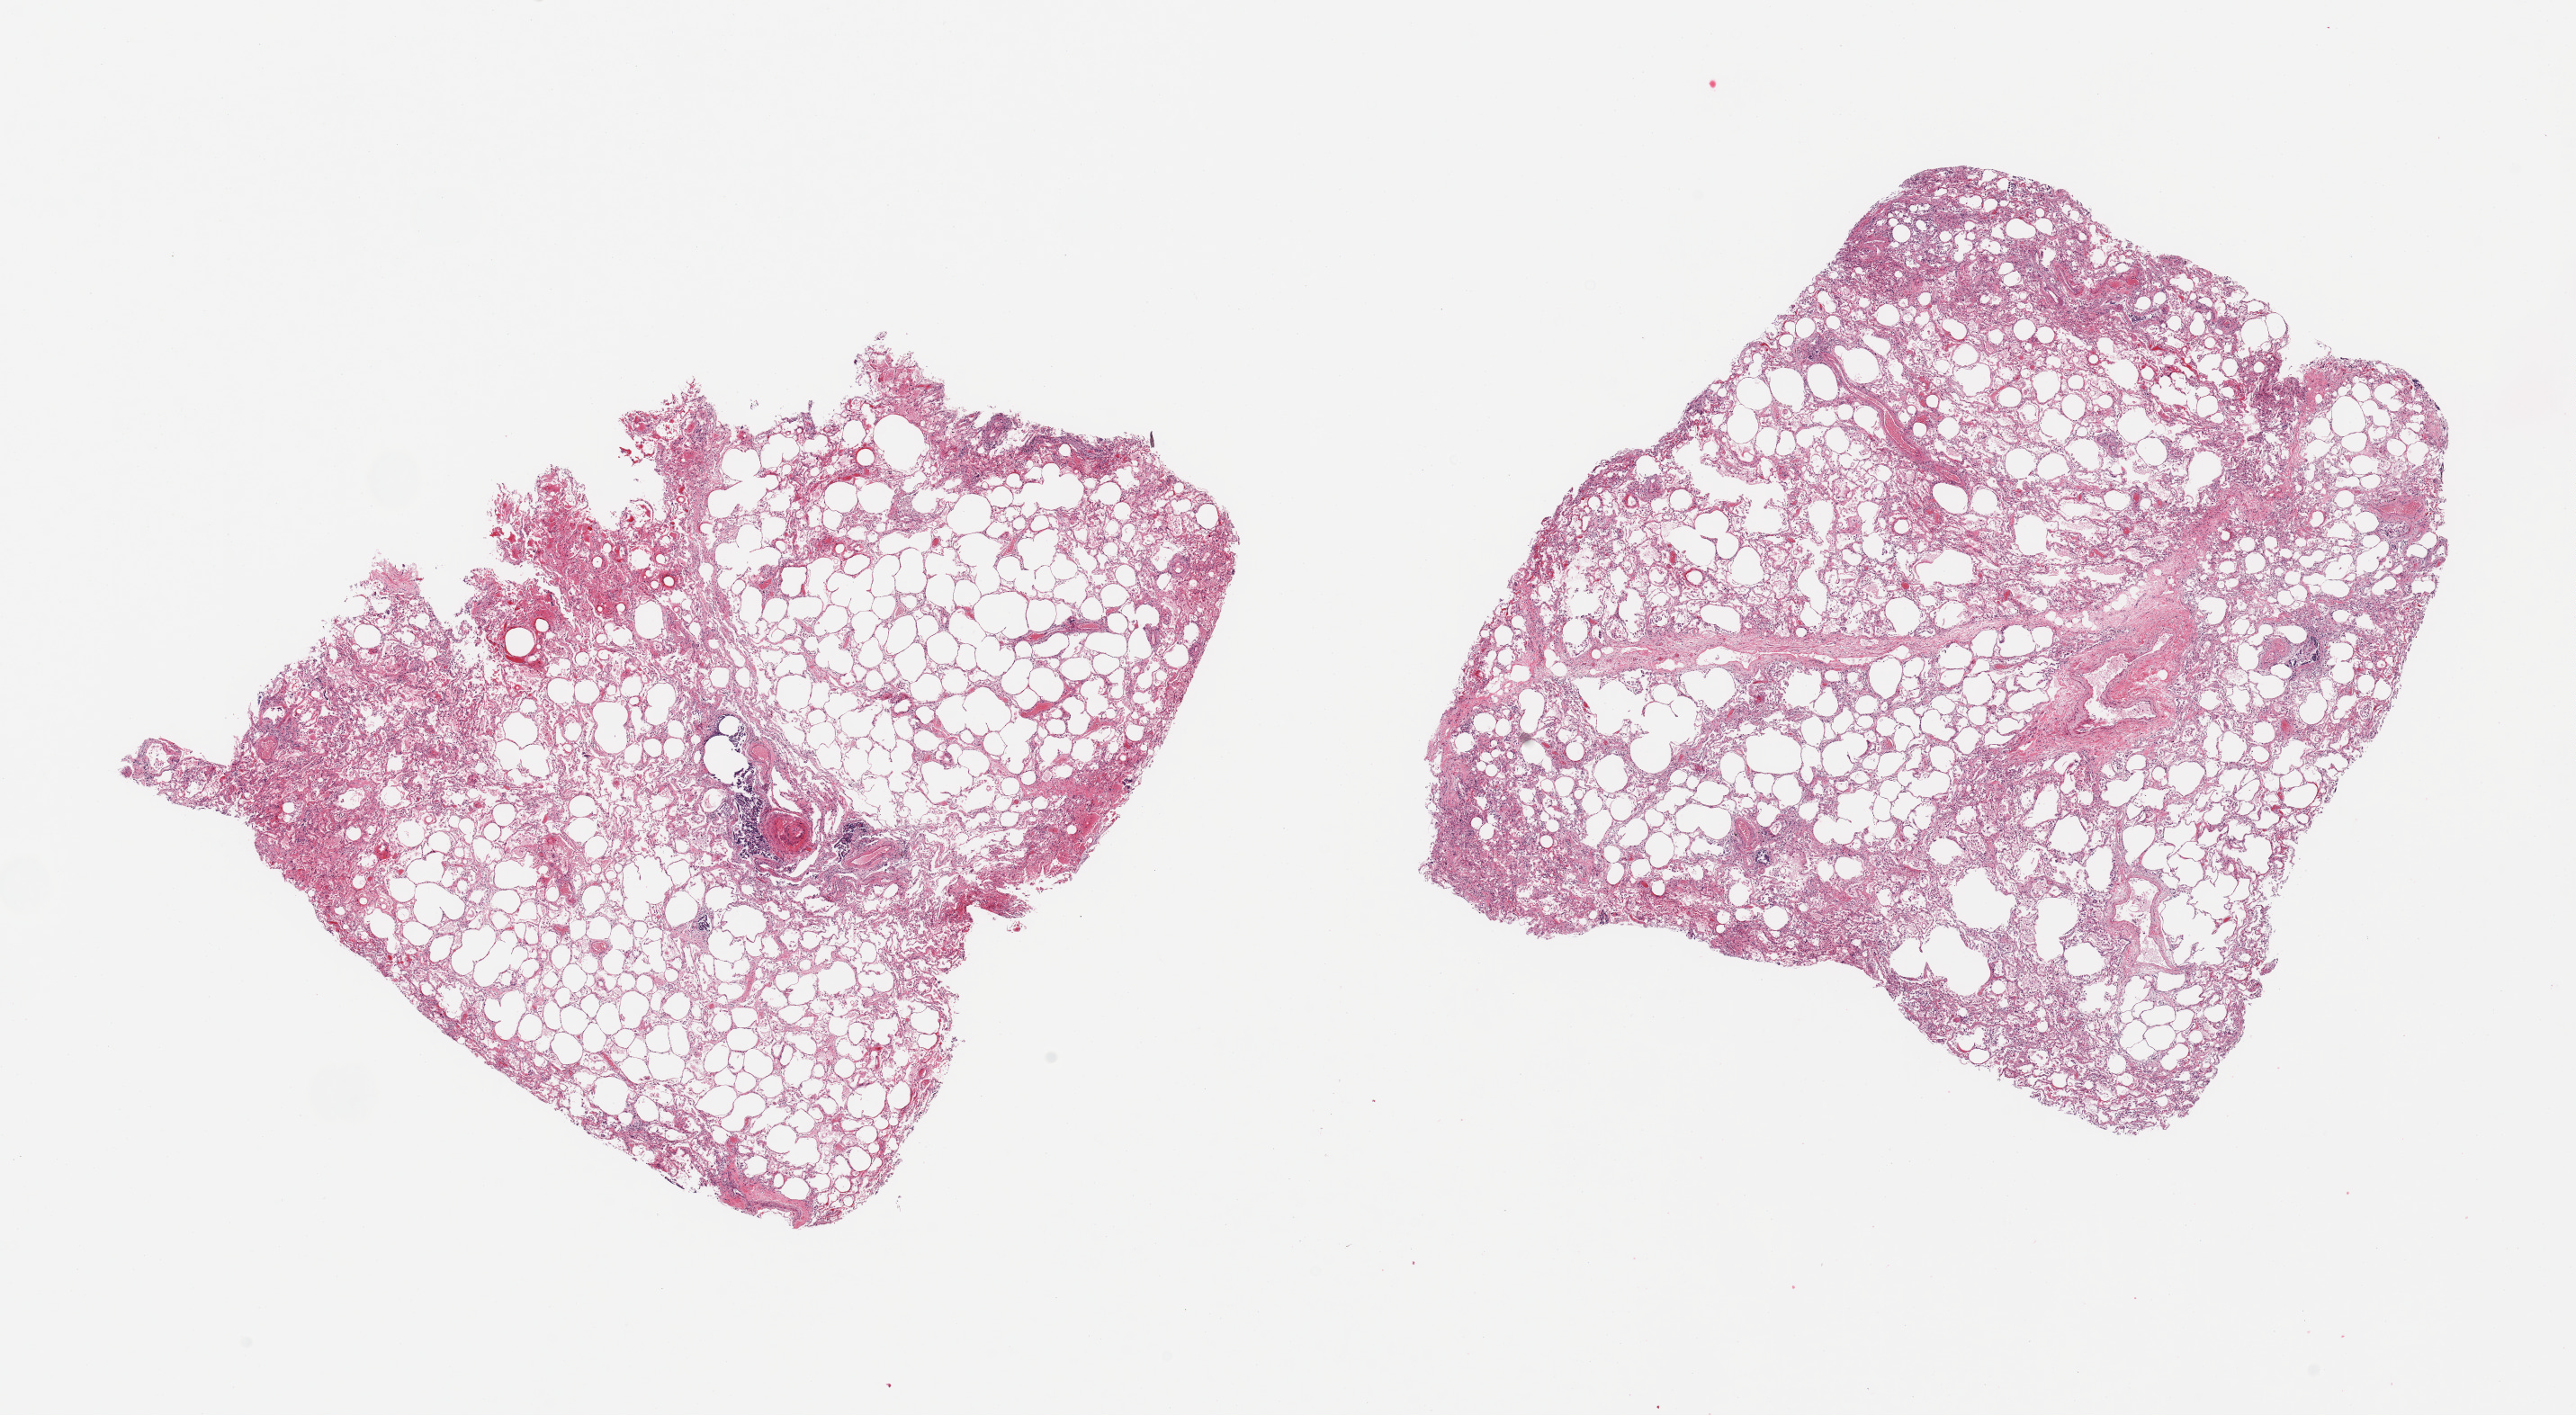
Haematoxylin and eosin whole-slide image, low-resolution overview of the scanned area, about 22.6 x 12.4 mm (acquisition: 20x scan); PAXgene-fixed, paraffin-embedded tissue; target tissue: lung; tissue donor sample. Donor: female.
- reviewer comment on this tissue sample: 2 pieces; mild emphysema